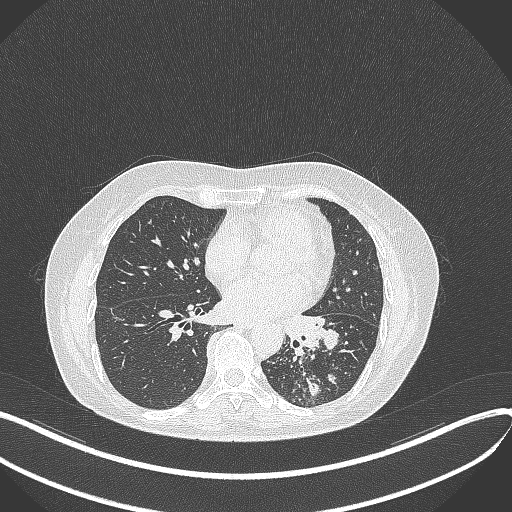
Chest CT, one axial slice; position 179 of 429 along the scan axis; reconstruction kernel B70f; 100 kVp; lung window (W 1500 / L -600 HU); 1 mm slice thickness; 512 × 512 image matrix. Patient: female, 63 years. Case-level facts recorded for this patient, not image findings: clinical TNM (as recorded): T1b N0 M0.
Outlined on this slice (rectangle marked by the reading radiologist):
- lung tumour (recorded histology: adenocarcinoma): bounding box <274,308,341,361> (left, top, right, bottom; pixels)